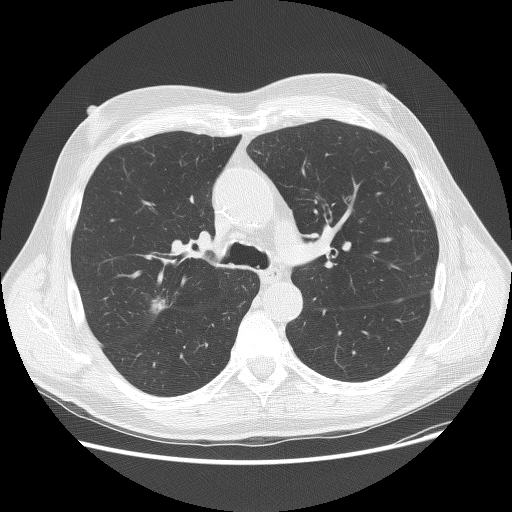
Chest CT (low-dose screening protocol), one axial image. Baseline annual screen. Lung window (W 1500 / L -600 HU). 2.5 mm slice thickness. 512 × 512 image matrix, field of view 380 × 380 mm. Male, age 70 years at enrolment.
- Expert reader's lesion annotation, bounding box [x1, y1, x2, y2] px = [134, 277, 198, 333].
- The screening reader recorded 2 non-calcified nodules or masses ≥4 mm on this exam (right upper lobe, left lower lobe); which of them this box marks is not recorded.
- Later outcome: lung cancer diagnosed 15 days after this screen — adenocarcinoma, NOS, right upper lobe, poorly differentiated (G3), stage IIA (AJCC 6th edition), 23 mm at pathology.